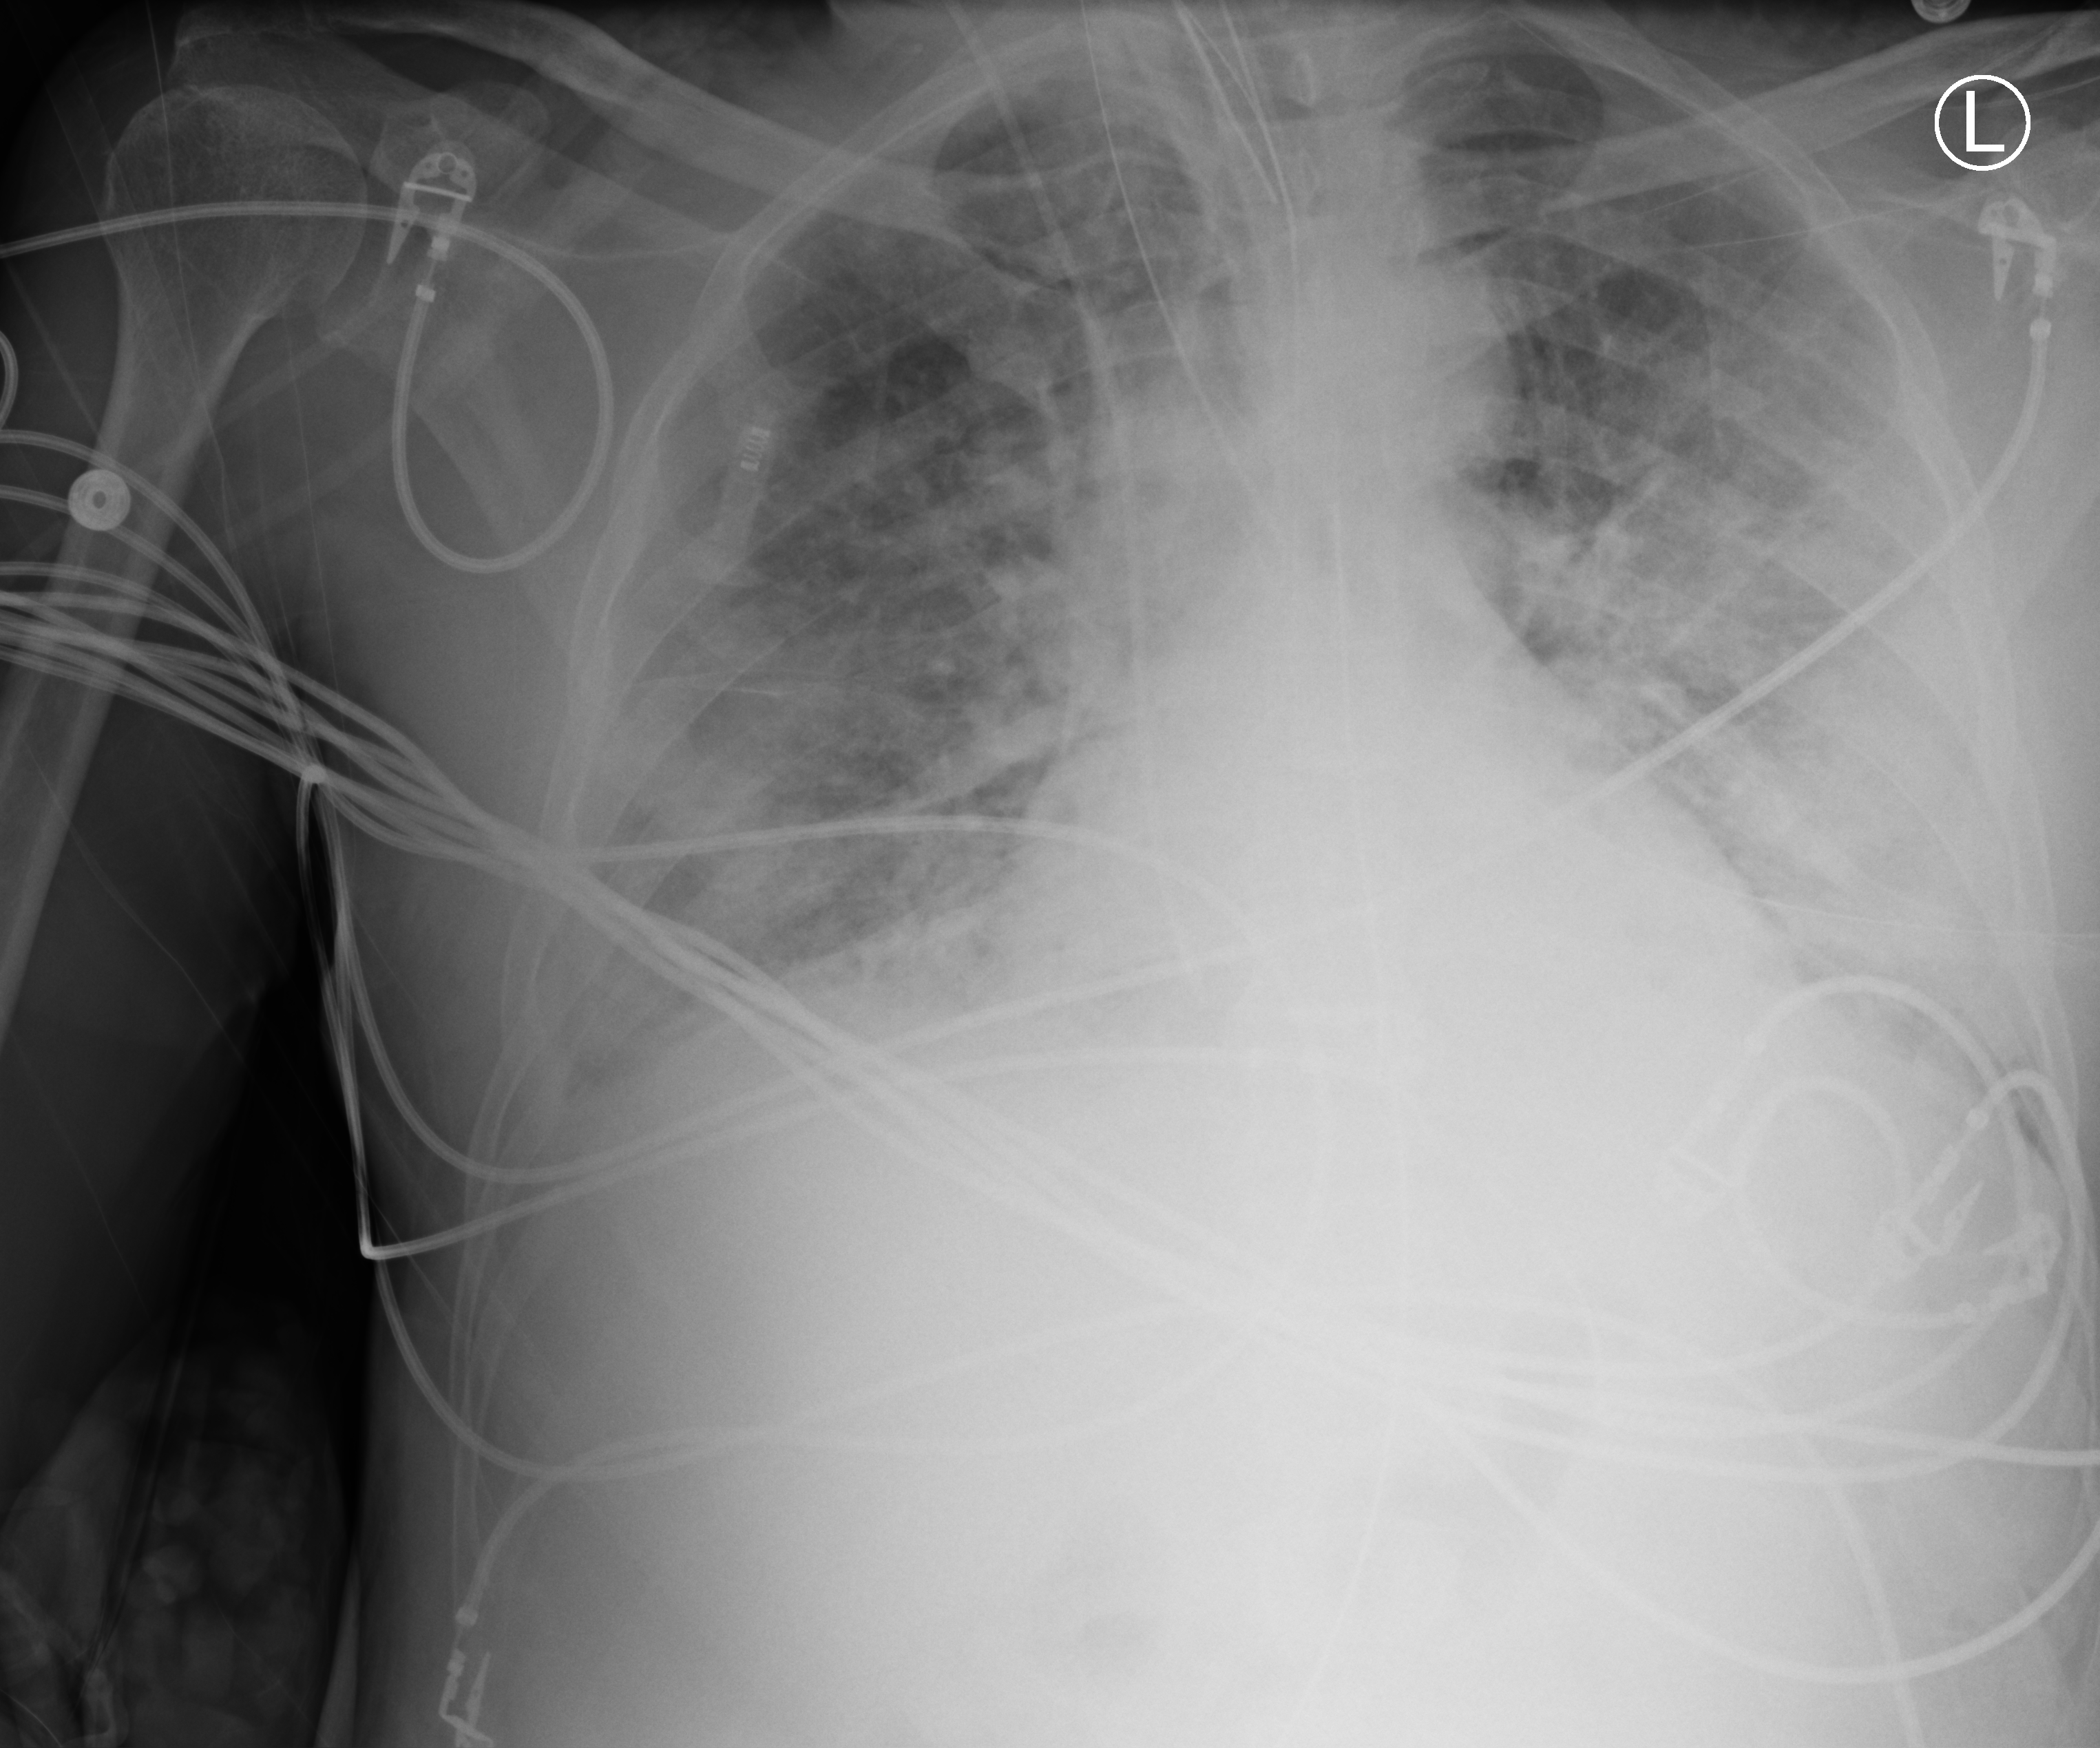
Bedside chest radiograph (computed radiography); anteroposterior (AP) projection. Male patient hospitalised with COVID-19, age 18–59 years.
Hospital-stay facts (about this admission, not read from this image; timing relative to this image not recorded): other chronic lung disease (admission record): no; mechanically ventilated during this hospital stay: yes.